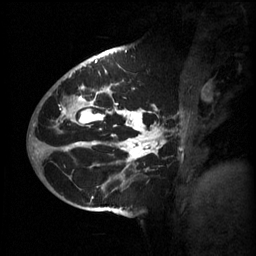
Breast MRI (dynamic contrast-enhanced), one sagittal slice; position 35 of 60 along the scan axis; 3 images stored at this slice position (order not interpretable as contrast timing); 1.5 T; TE 4.2 ms, TR 11 ms; 2 mm slice thickness; 256 × 256 image matrix, field of view 220 × 220 mm. Female patient, age 51 years.
Annotated regions visible in this slice (semi-automatic segmentation, software-assisted and operator-edited):
- analysis volume of interest (the breast-tissue region the enhancement analysis was run in; not a lesion): bounding box [x1, y1, x2, y2] px = [63, 80, 186, 201]
- tumour enhancement mask (voxels above the 70 % enhancement threshold inside the analysis volume of interest): [63, 84, 166, 199]